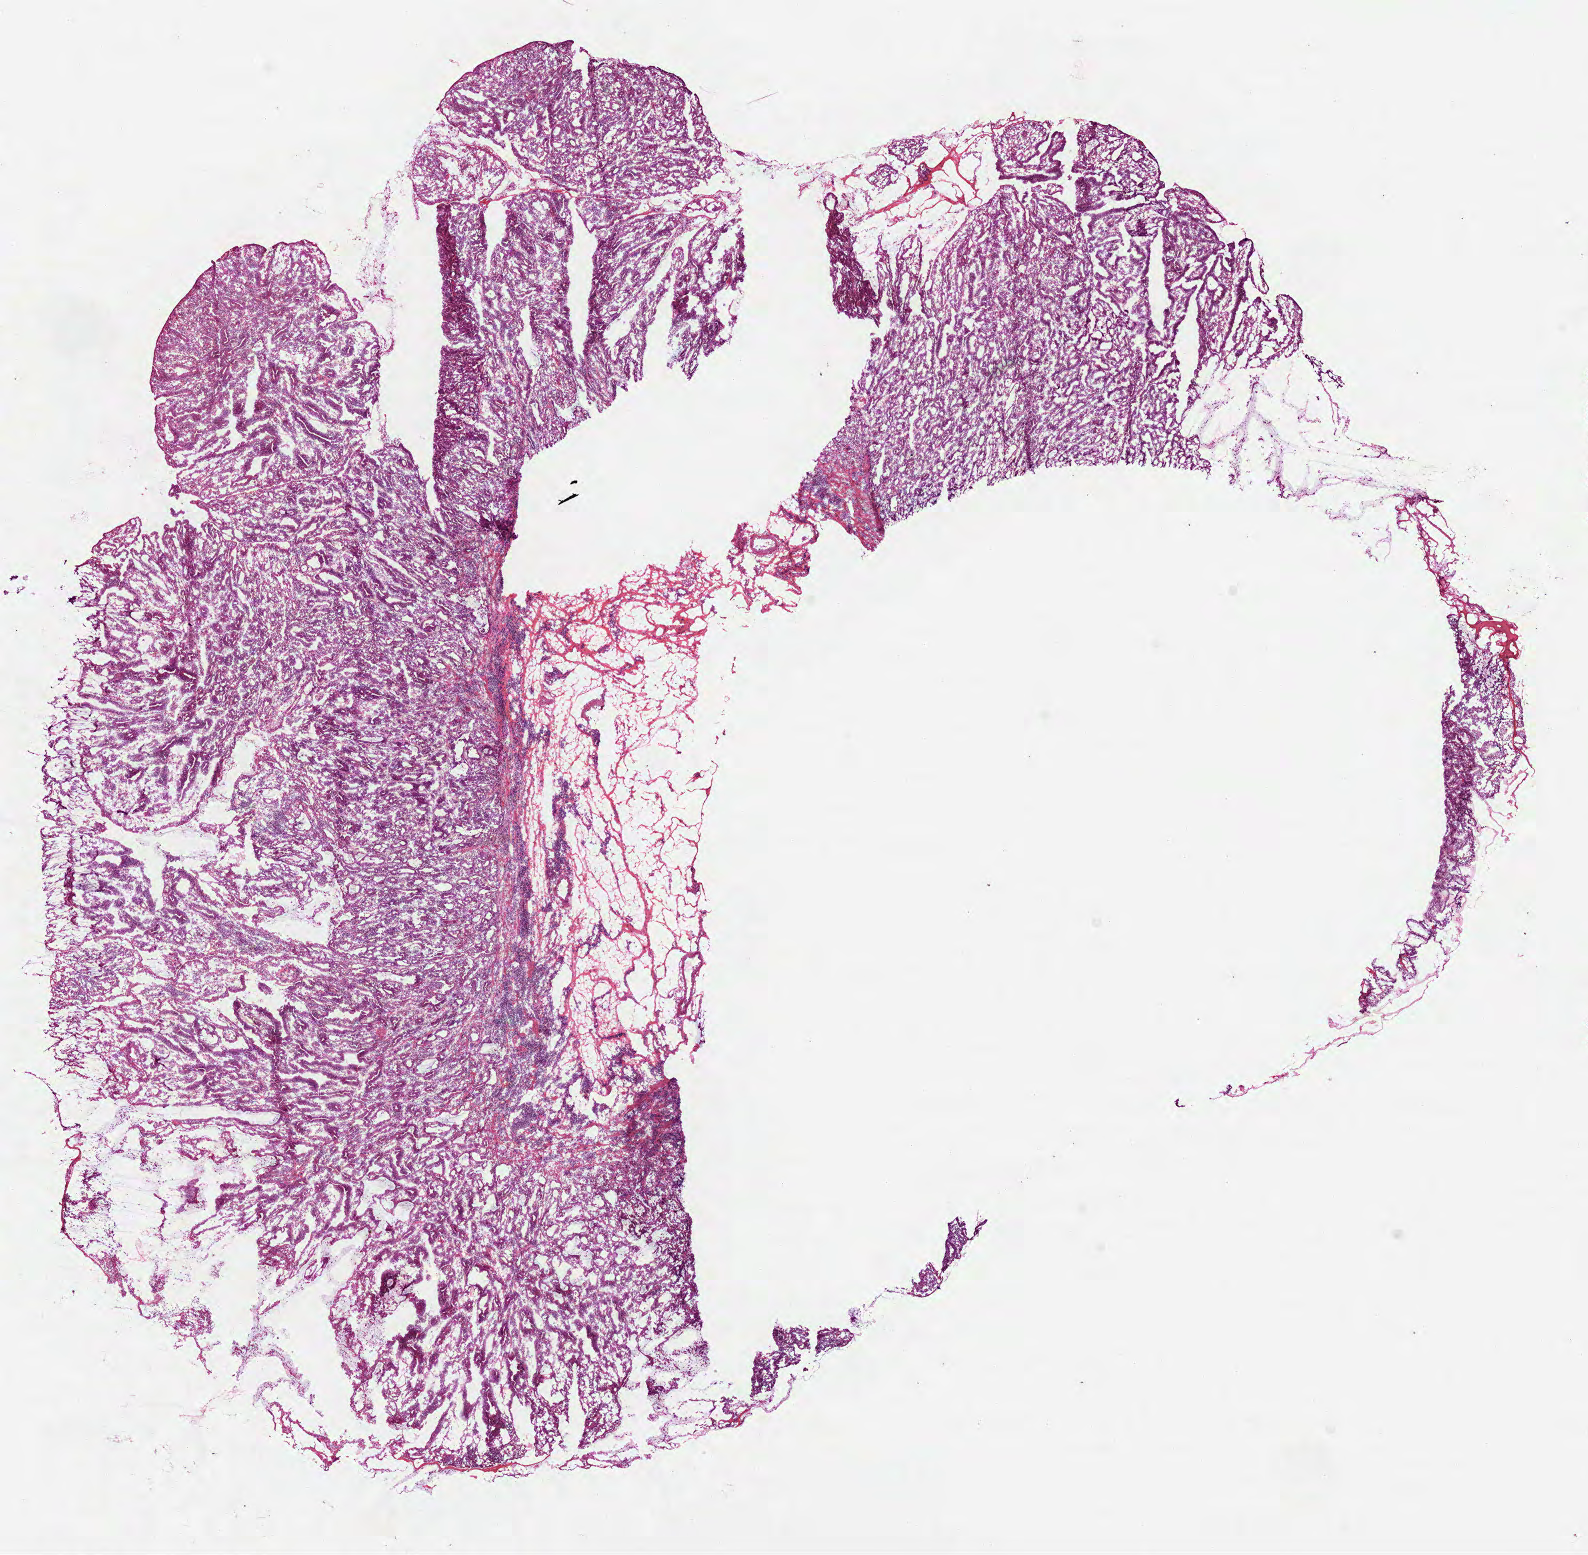
H&E whole-slide image, a low-resolution overview of the entire scanned area, about 12.8 x 12.5 mm (slide scanned at 40x). Frozen section from the bottom of the tissue portion. Primary tumour sample from the stomach. Male, age 81 years at initial diagnosis. Histologic grade: G2 (moderately differentiated). Pathologist review of this section (percent, as recorded): tumour cells 85%, tumour nuclei 78%, normal cells 0%, stromal cells 15%, necrosis 0%. Inflammatory infiltration, as recorded: lymphocyte infiltration 15%.
AJCC pathologic stage: IA (7th edition). Lymph nodes positive (case pathology): 0 of 4 examined. Diagnosis: Papillary adenocarcinoma, NOS (body of stomach). TNM: T1b N0 M0.